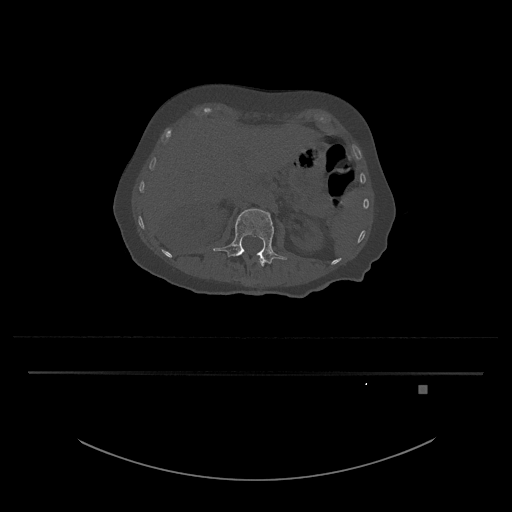
CT including the spine, one axial slice. Reconstruction kernel Br40s/3. 120 kVp. Bone window (W 1800 / L 400 HU). 0.5 mm slice thickness. 512 × 512 image matrix. Female patient, age 57 years. Case-level facts recorded for this patient, not image findings: primary cancer: cervical.
Outlined on this slice (semi-automatic segmentation, software-assisted and operator-edited):
- L1 vertebra: box from (x=244, y=251) to (x=265, y=266) px